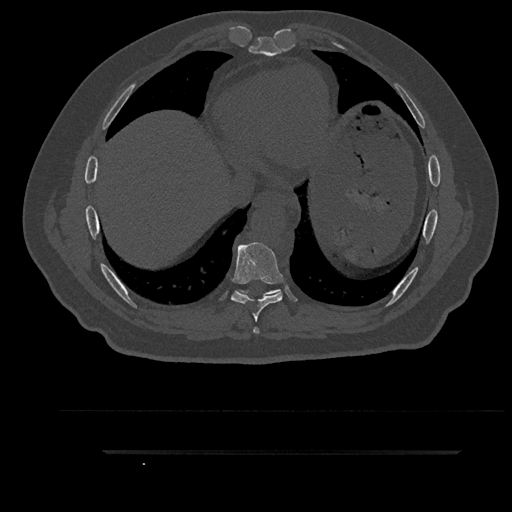
CT including the spine, one axial slice. Position 466 of 797 along the scan axis. 120 kVp. Bone window (W 1800 / L 400 HU). 0.5 mm slice thickness. 512 × 512 image matrix. Male patient, age 63 years. From the clinical record (not read from this slice): primary cancer: renal; vertebrae with lytic lesions (as recorded): T8.
Annotated regions visible in this slice (semi-automatically segmented with operator editing):
- T7 vertebra: bounding box (x1, y1, x2, y2) in pixels: (253, 327, 259, 334)
- T8 vertebra: (231, 242, 283, 322)
- T9 vertebra: (238, 289, 281, 296)